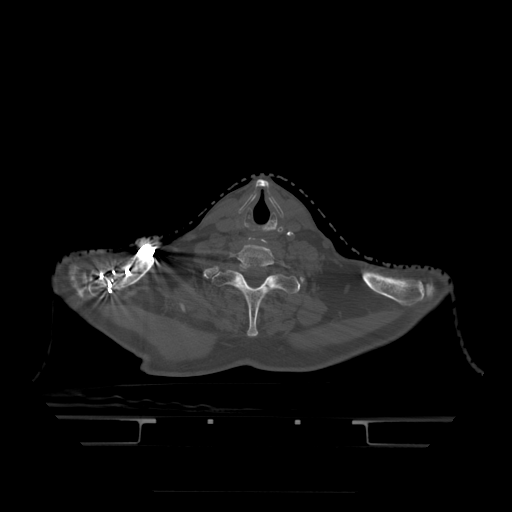
CT including the spine, one axial slice. Bone window (W 1800 / L 400 HU). 1.25 mm slice thickness. 512 × 512 image matrix, field of view 436 × 436 mm. Patient age 68 years. From the clinical record (not read from this slice): primary cancer: urothelial.
Outlined on this slice (semi-automatically segmented with operator editing):
- T1 vertebra: bounding box [x1, y1, x2, y2] px = [213, 266, 301, 337]